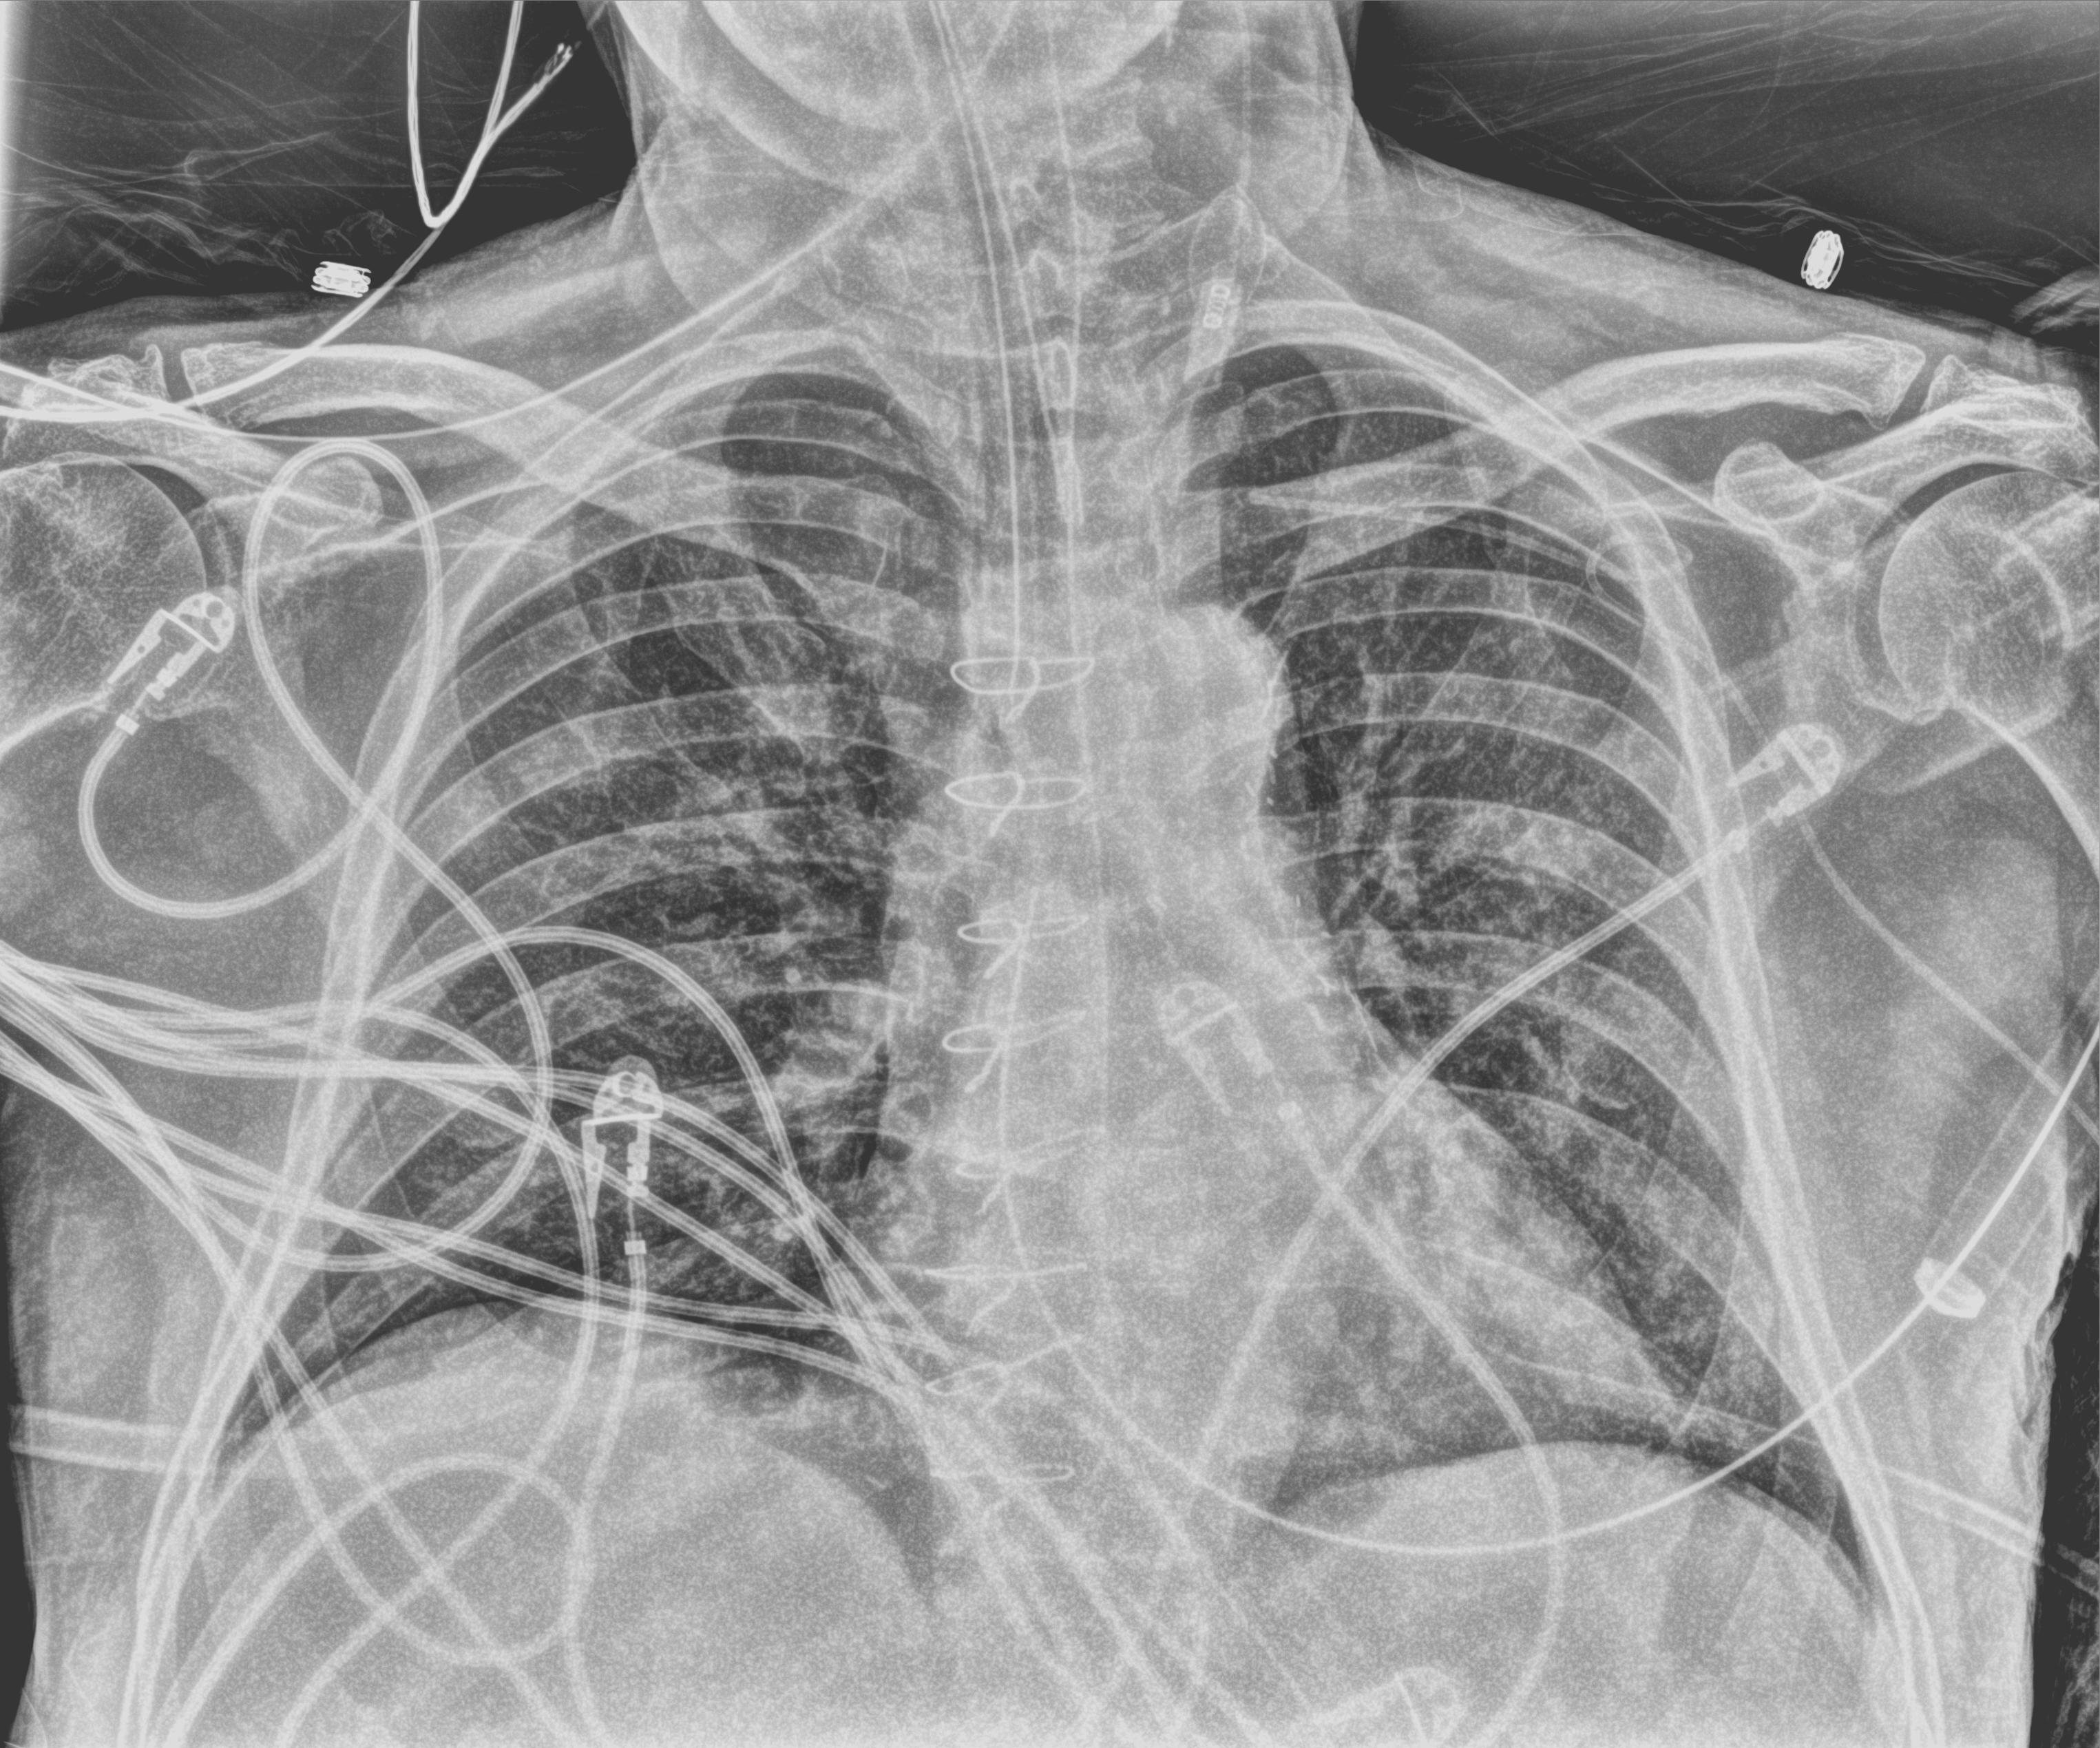
Chest X-ray (portable), anteroposterior (AP) projection. Patient hospitalised with COVID-19; male, aged 60–74 years.
From the hospital-stay record, not from the radiograph (when in the stay this image was taken is not recorded): mechanically ventilated during this hospital stay: yes.